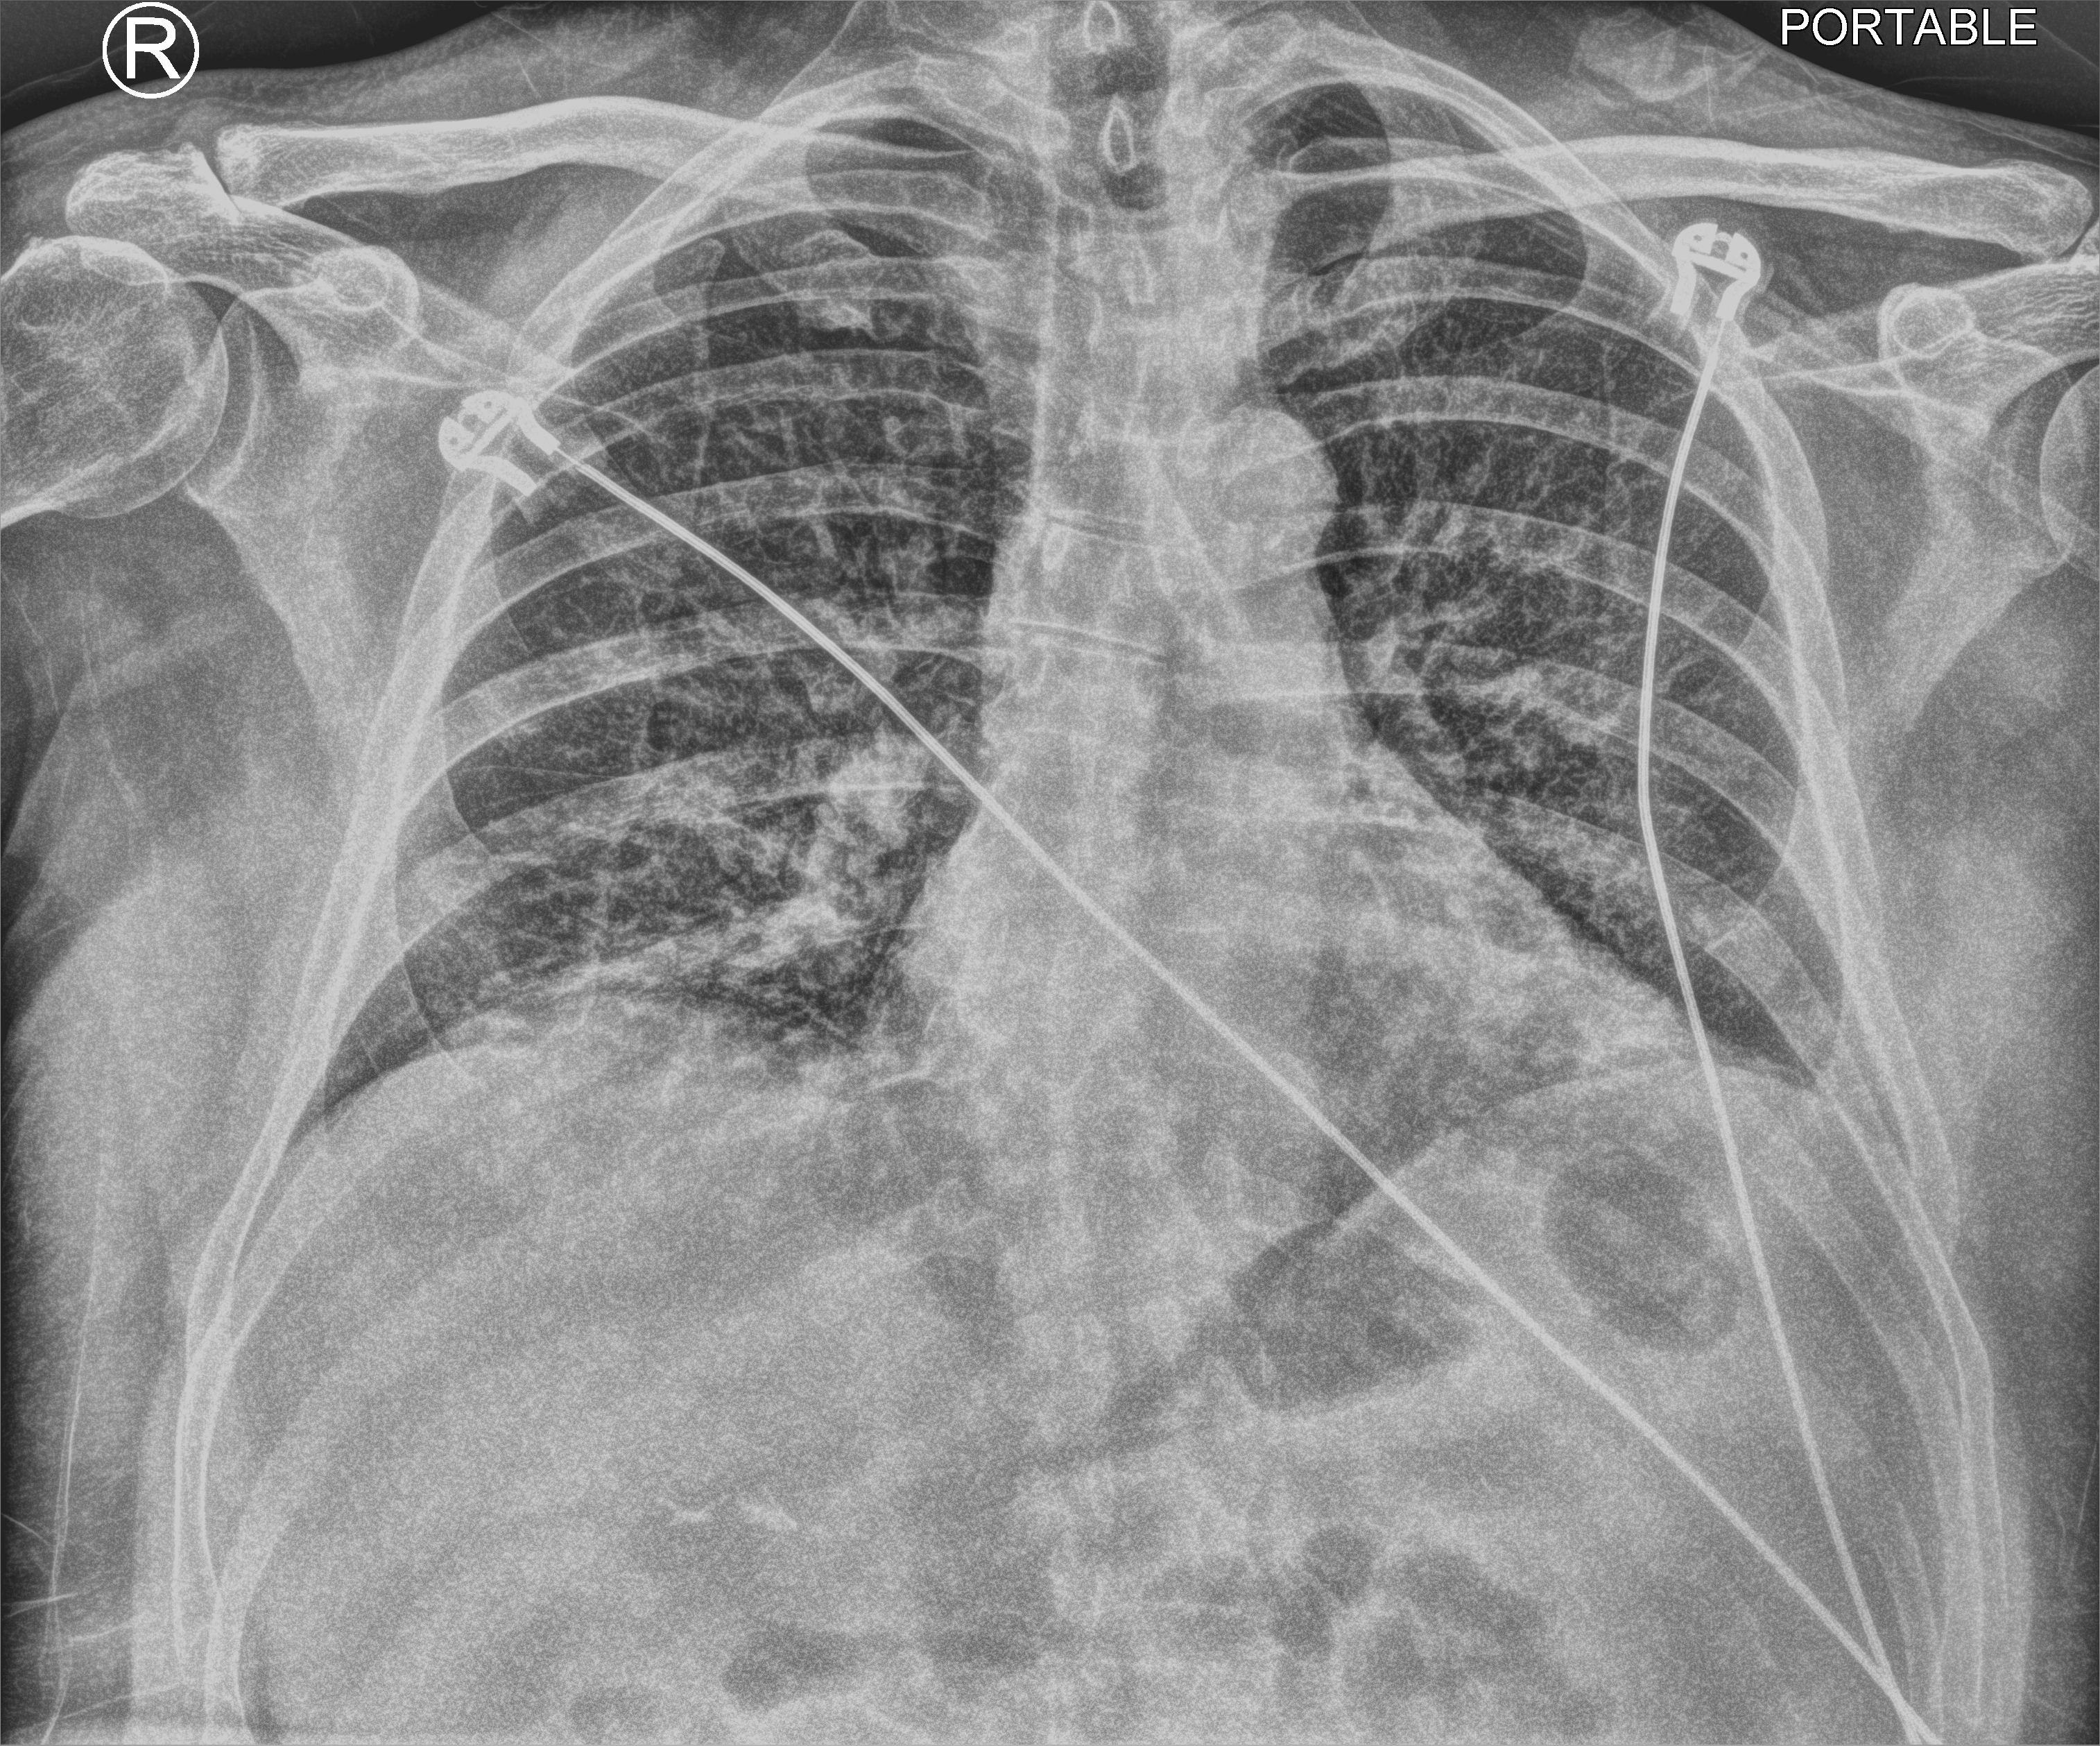
Chest X-ray (portable); anteroposterior (AP) projection. Male patient hospitalised with COVID-19, age 60–74 years.
Admission-level facts for this patient (not findings on this image; timing relative to this image not recorded): length of hospital stay: 9 days.